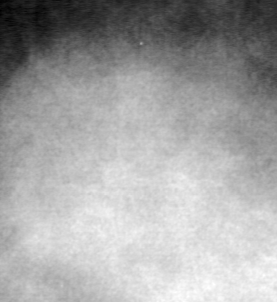
Cropped region of a digitized screen-film mammogram centred on a radiologist-marked abnormality, left breast, CC view, BI-RADS breast density category 3 (scale 1–4).
- Finding: mass, shape lobulated, margins ill defined; BI-RADS assessment category 4; pathology result (as recorded, not read from the image): malignant.